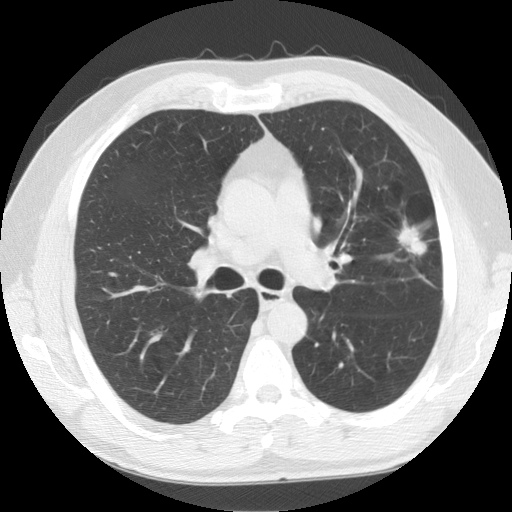
Low-dose screening chest CT, one axial slice. Position 91 of 141 along the scan axis. Reconstruction kernel STANDARD. Lung window (W 1500 / L -600 HU). 2.5 mm slice thickness. 512 × 512 image matrix.
Structures marked on this image (manually delineated by an expert):
- lesion 1 (tumor, upper lobe of left lung): bounding box [x1, y1, x2, y2] px = [397, 225, 427, 255]